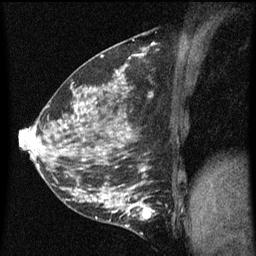
Breast MRI (dynamic contrast-enhanced), one sagittal slice; position 25 of 60 along the scan axis; dynamic contrast-enhanced series, image 2 of 5 at this slice position (ordered by acquisition); 1.5 T; TE 4.2 ms, TR 8 ms; 2 mm slice thickness; 256 × 256 image matrix. Patient: female, 35 years.
Annotated regions visible in this slice (semi-automatically segmented with operator editing):
- analysis volume of interest (the breast-tissue region the enhancement analysis was run in; not a lesion): bounding box (x1, y1, x2, y2) in pixels: (118, 190, 157, 229)
- tumour enhancement mask (voxels above the 70 % enhancement threshold inside the analysis volume of interest): (118, 196, 156, 227)